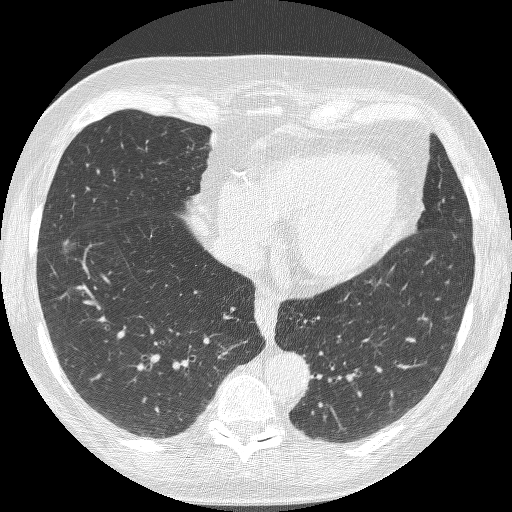
Axial slice from a low-dose chest CT screening exam; baseline screening round; lung window (W 1500 / L -600 HU); 1.25 mm slice thickness; 512 × 512 image matrix. Female participant, aged 68 years at enrolment. Current smoker at enrolment.
Lesion marked by an expert reader, bounding box (x1, y1, x2, y2) in pixels: (31, 228, 84, 284). The exam's reader record, not a measurement of the box and not confirmed to be the same lesion: non-calcified nodule or mass ≥4 mm, right lower lobe, 16 × 12 mm, poorly defined margins, ground glass attenuation. Official screen result: positive, change unspecified: nodule(s) >= 4 mm or enlarging nodule(s), mass(es), or other non-specific abnormalities suspicious for lung cancer. Participant outcome: lung cancer diagnosed 406 days after this screen — bronchiolo-alveolar adenocarcinoma, NOS, right lower lobe, well differentiated (G1), stage IA (AJCC 6th edition), 13 mm at pathology.